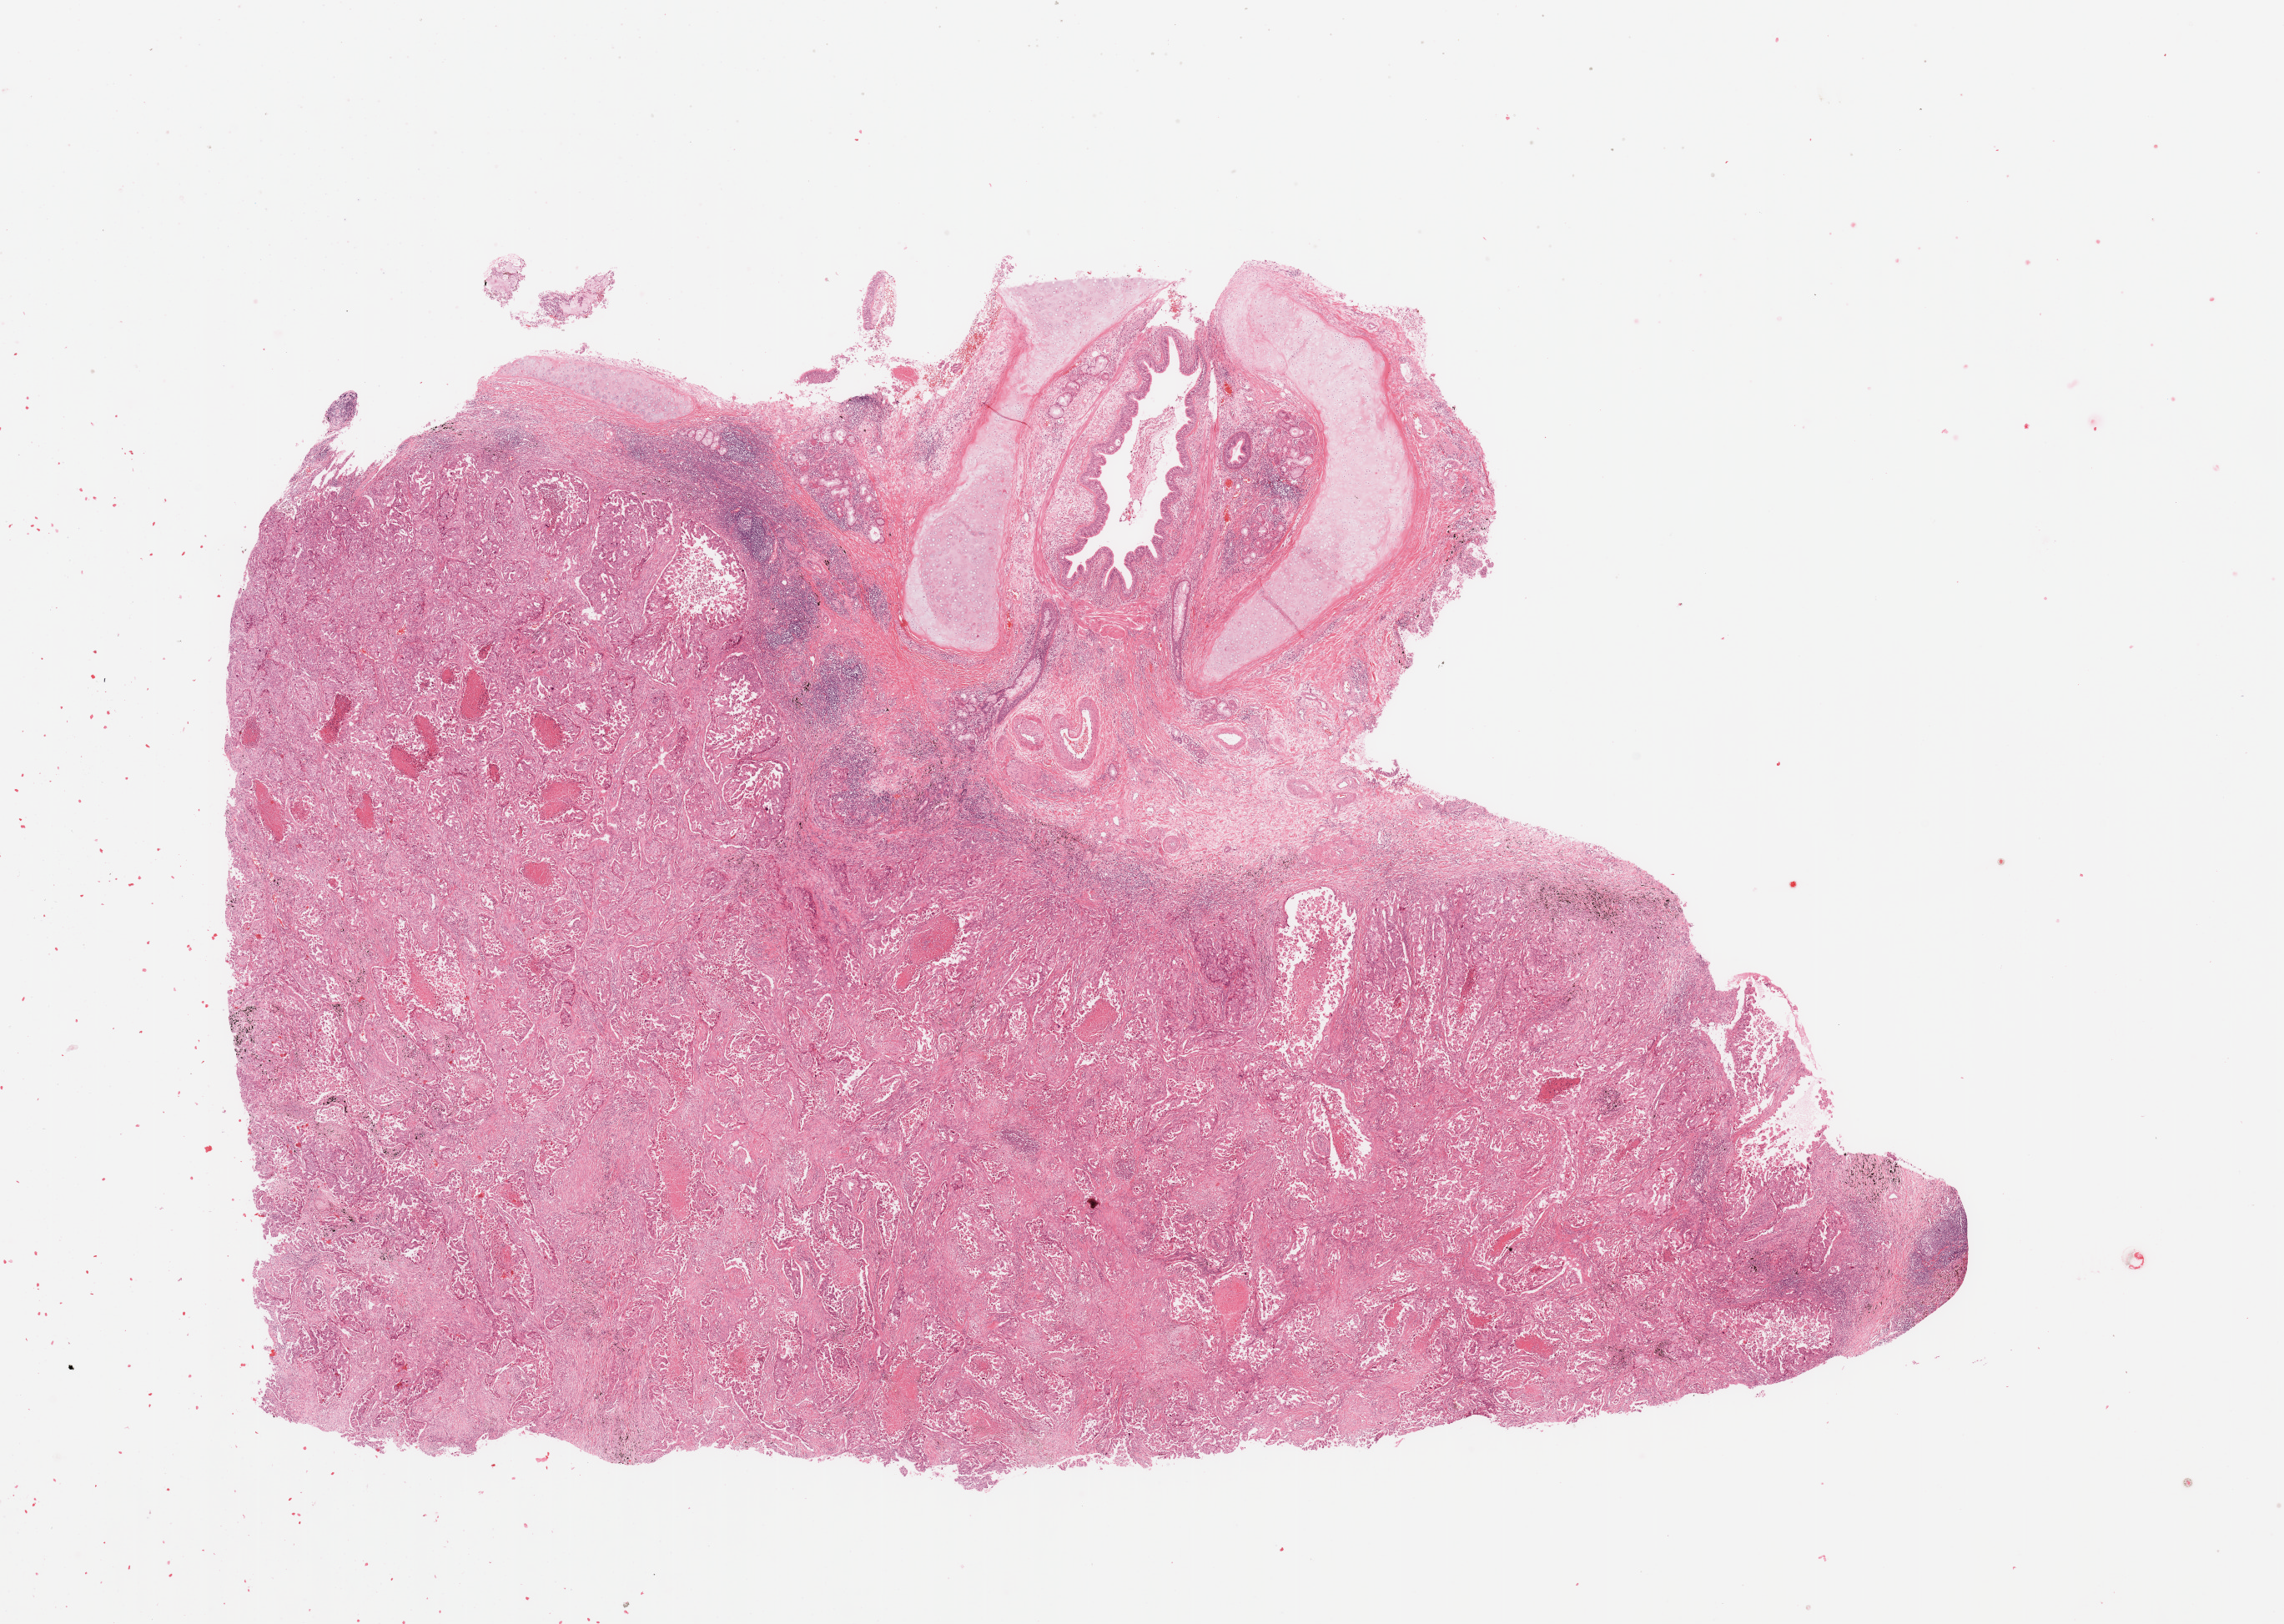
H&E-stained whole-slide image — shown as a low-resolution overview of the whole scanned area (about 21.7 x 15.4 mm); lung, tumour tissue. Male, 56 y/o. Histologic grade: G3 (poorly differentiated).
Diagnosis: Adenocarcinoma, NOS. Primary tumour site (as recorded): right upper lobe. AJCC pathologic stage: IB.